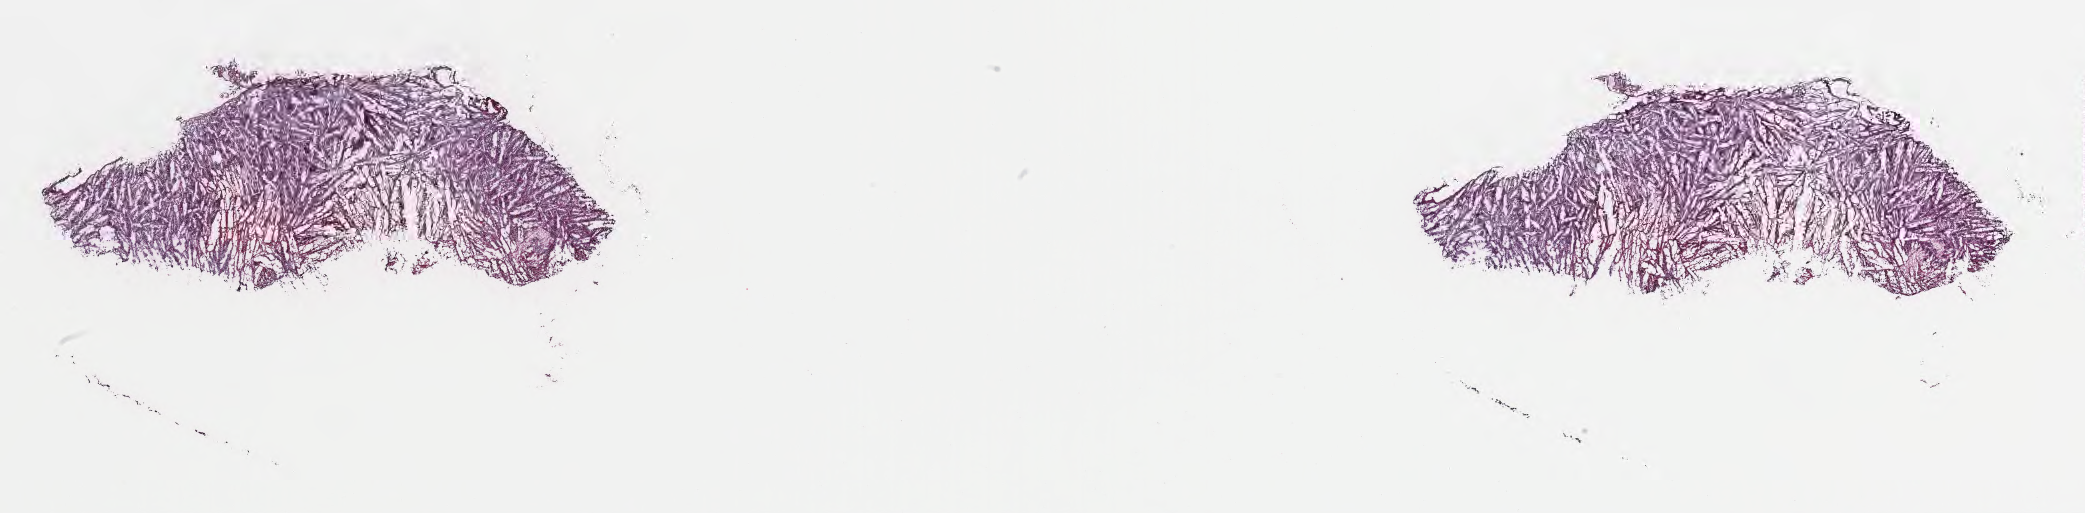
Digitized hematoxylin and eosin (H&E)-stained section of tumor tissue from the cerebellum — shown as a low-resolution overview of the whole scanned area (about 33.7 x 8.3 mm); cryosection (OCT / tissue freezing medium). Male patient, age 180 months (15 years).
• recorded diagnosis: Large cell medulloblastoma